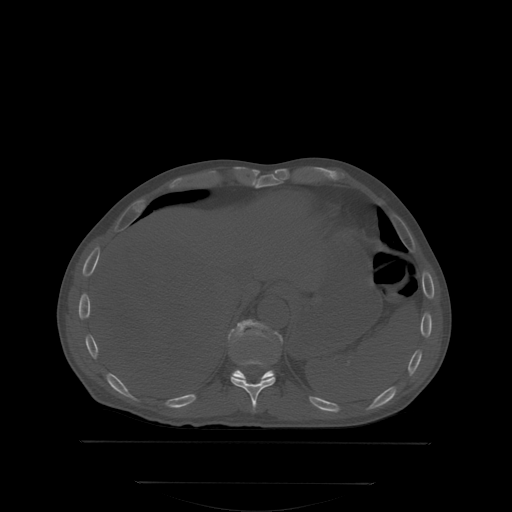
CT including the spine, one axial slice. Position 189 of 350 along the scan axis. Bone window (W 1800 / L 400 HU). 512 × 512 image matrix. Patient: male, 58 years. From the clinical record (not read from this slice): primary cancer: prostate; vertebrae with lytic lesions (as recorded): L1.
Outlined on this slice (semi-automatic segmentation, software-assisted and operator-edited):
- T10 vertebra: bounding box <231,358,276,412> (left, top, right, bottom; pixels)
- T11 vertebra: <229,320,281,381>